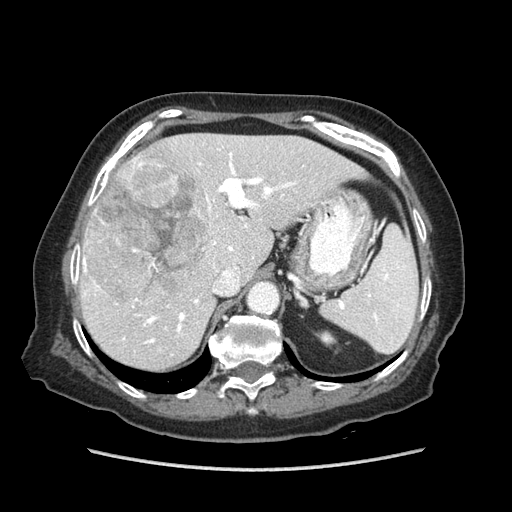
Contrast-enhanced abdominal CT (liver protocol), one axial slice. Position 56 of 89 along the scan axis. Reconstruction kernel STANDARD. 140 kVp. Soft-tissue window (W 400 / L 40 HU). 512 × 512 image matrix, field of view 360 × 360 mm. From the clinical record (not read from this slice): diagnosis: hepatocellular carcinoma (patient treated with transarterial chemoembolisation; whether this scan precedes or follows treatment is not stated here); TNM stage (as recorded): Stage-IIIA; Child-Pugh class: A; tumour differentiation: well differentiated; tumour nodularity: multinodular.
Structures marked on this image (semi-automatically segmented with operator editing):
- liver parenchyma outside the tumour (the mass and vessels are separate outlines, so this box may not span the whole liver): box from (x=78, y=134) to (x=367, y=370) px
- mass: (x=85, y=156)–(x=209, y=297)
- liver vessels: (x=78, y=153)–(x=295, y=344)